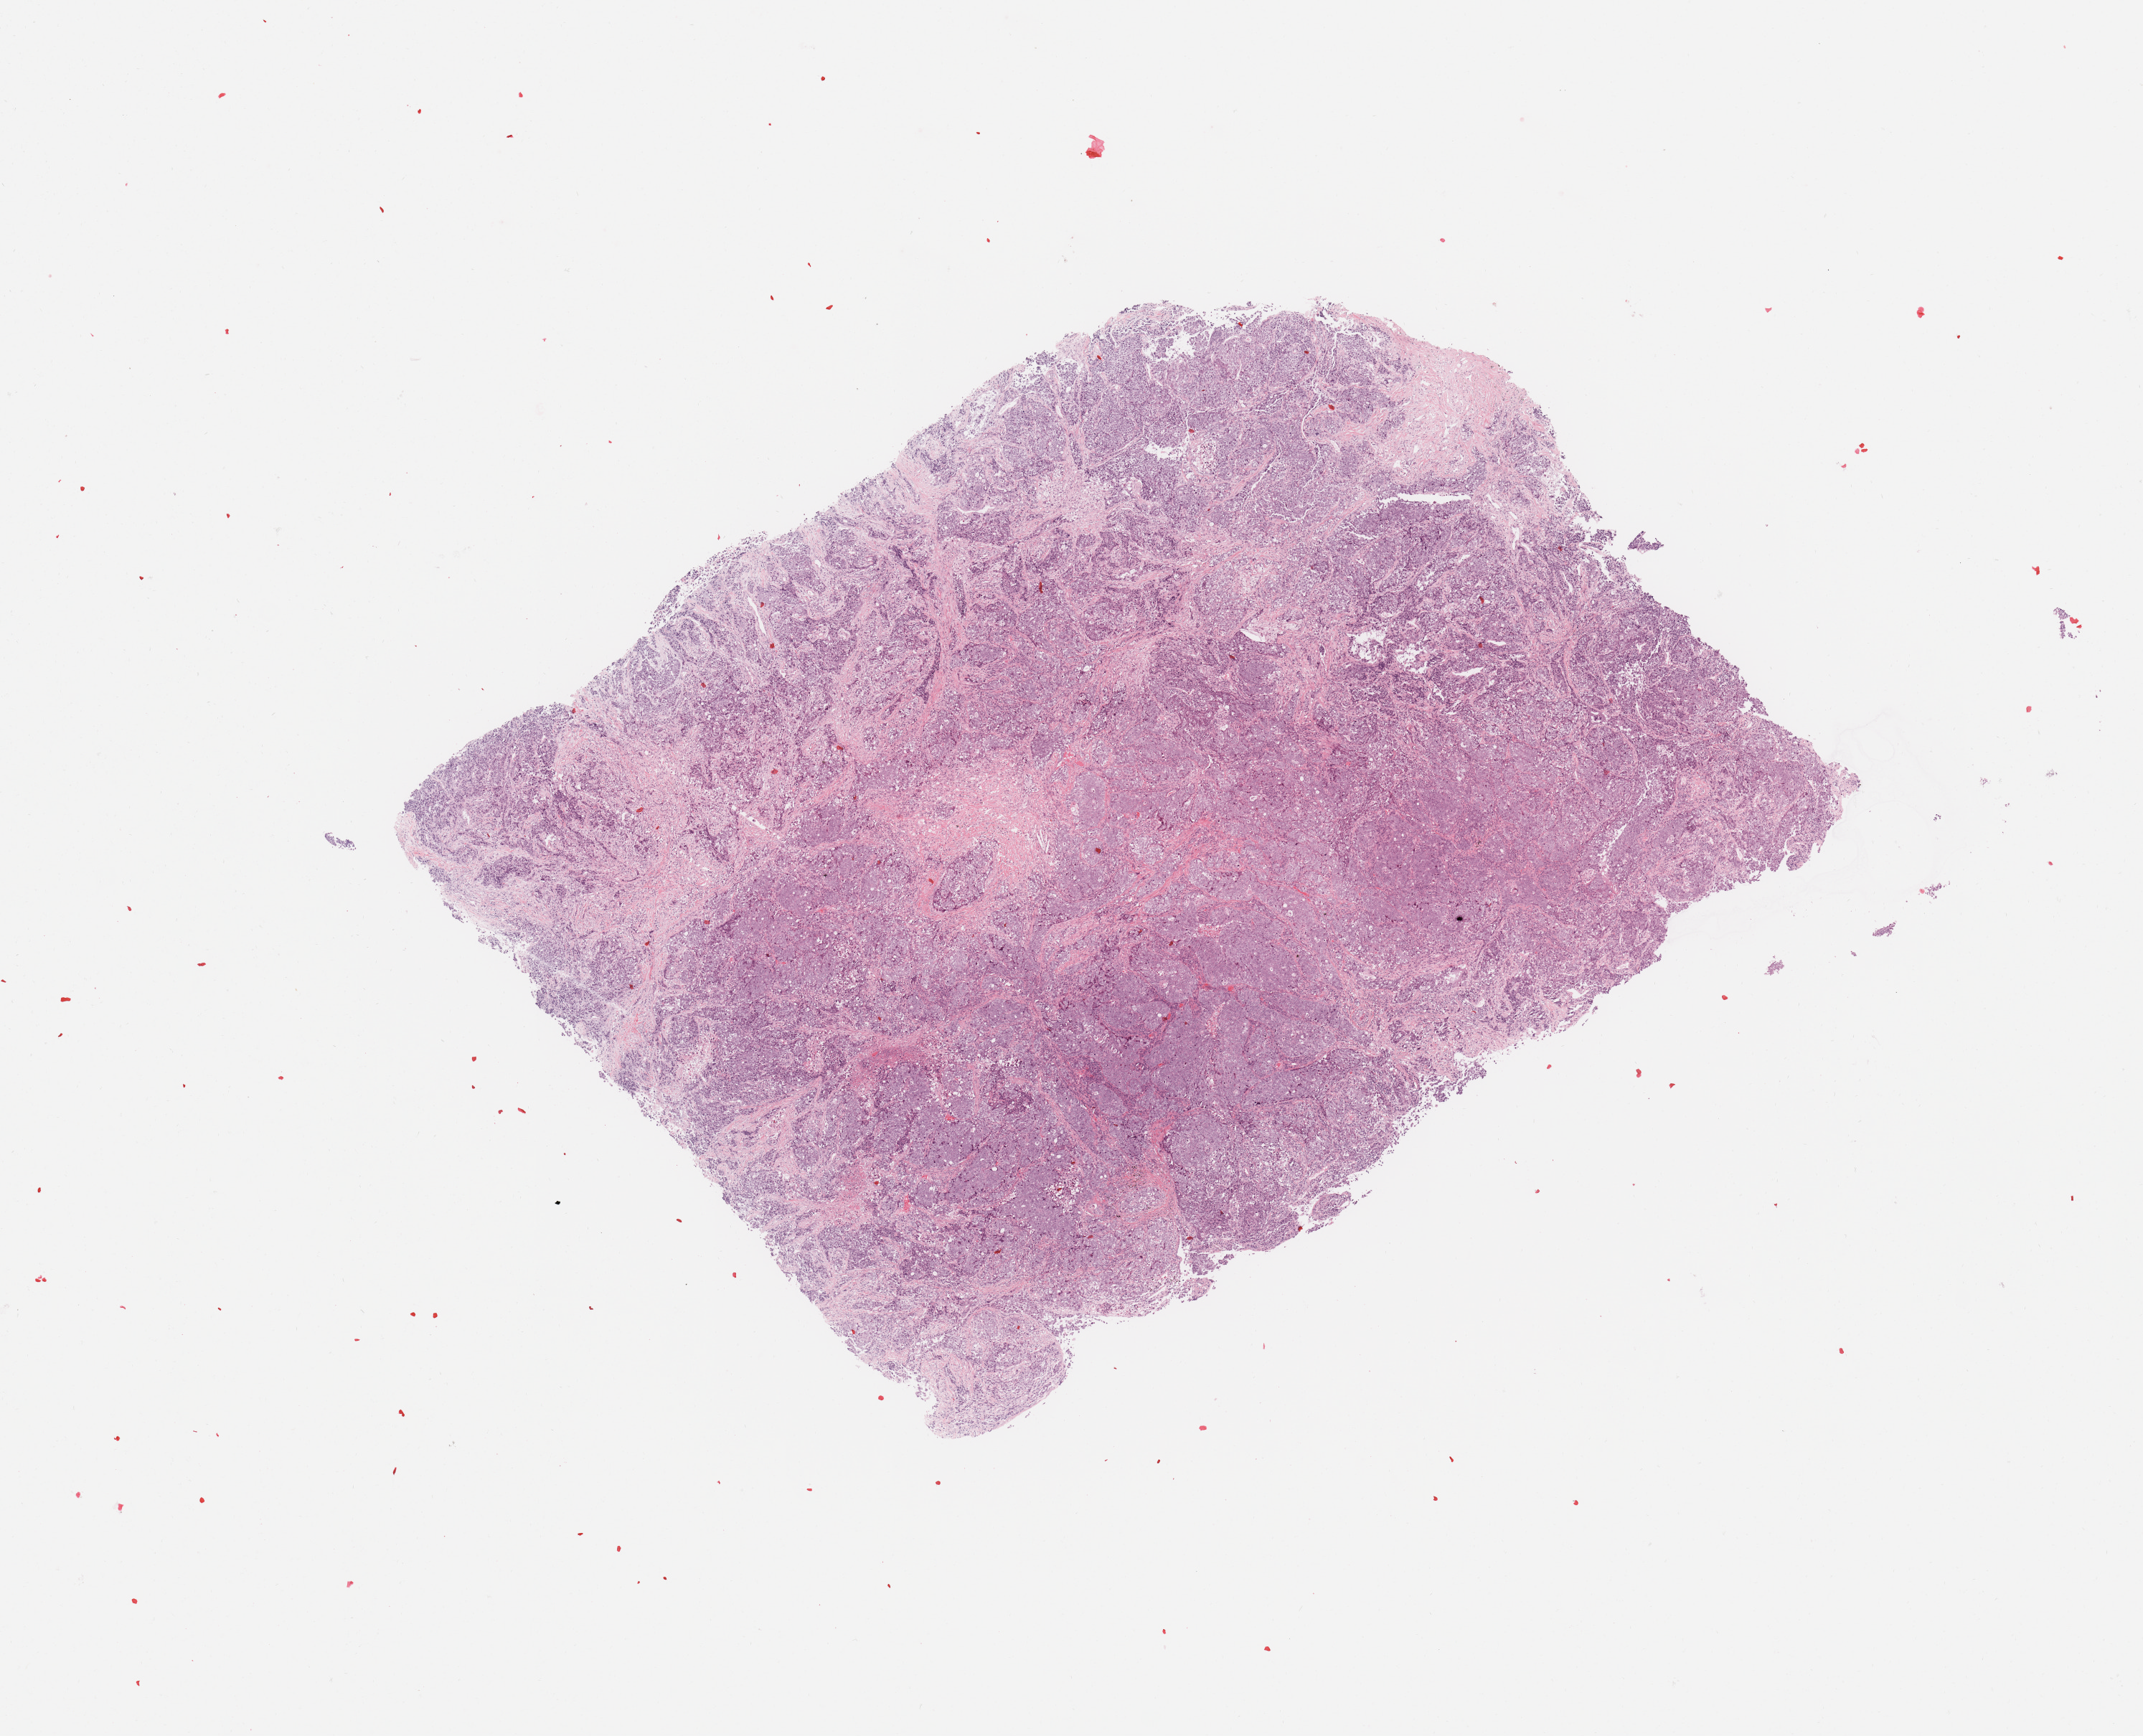
H&E whole-slide image, whole scanned area (about 11.8 x 9.6 mm, slide scanned at 20x) shown as a low-resolution overview, tumour tissue sample, sampled site: lung. Patient: male, age 44 years. Histologic grade: G3 (poorly differentiated). Slide review estimates, as recorded: tumour nuclei 85%, necrosis 5%.
- histologic diagnosis: Squamous cell carcinoma, NOS
- AJCC pathologic stage: IIB
- primary tumour site (as recorded): left upper lobe